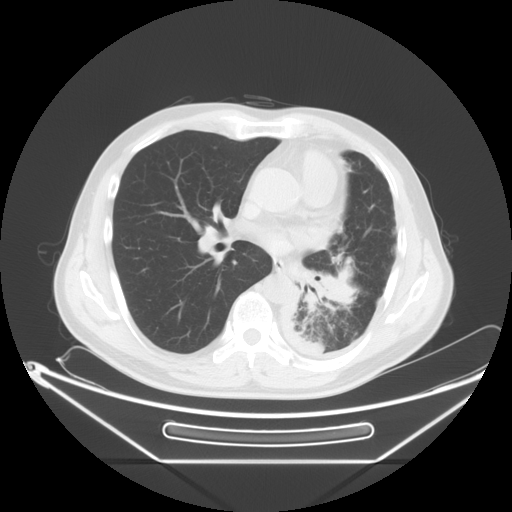
Chest CT, one axial slice; position 32 of 63 along the scan axis; 120 kVp; lung window (W 1500 / L -600 HU); 5 mm slice thickness; 512 × 512 image matrix. Male patient, age 60 years. From the clinical record (not read from this slice): clinical TNM (as recorded): T4 N1 M1.
Outlined on this slice (rectangle marked by the reading radiologist):
- lung tumour (recorded histology: adenocarcinoma): bounding box (x1, y1, x2, y2) in pixels: (304, 259, 363, 323)